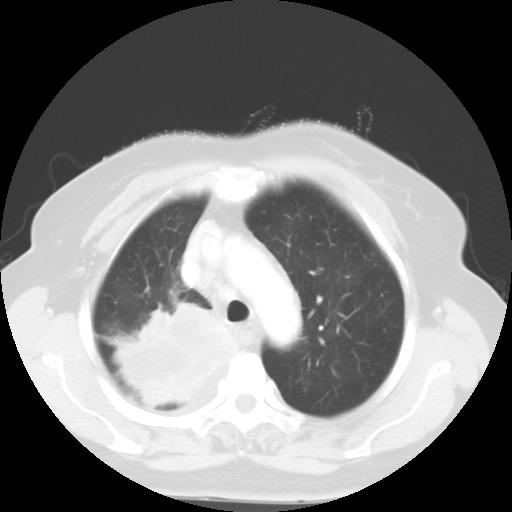
Chest CT, one axial slice; reconstruction kernel STANDARD; lung window (W 1500 / L -600 HU); 5 mm slice thickness; 512 × 512 image matrix, field of view 333 × 333 mm. Female patient, age 81 years. Case-level facts recorded for this patient, not image findings: clinical TNM (as recorded): T4 N3 M1b.
Structures marked on this image (rectangle marked by the reading radiologist):
- lung tumour (recorded histology: adenocarcinoma): bounding box [x1, y1, x2, y2] px = [110, 295, 240, 411]